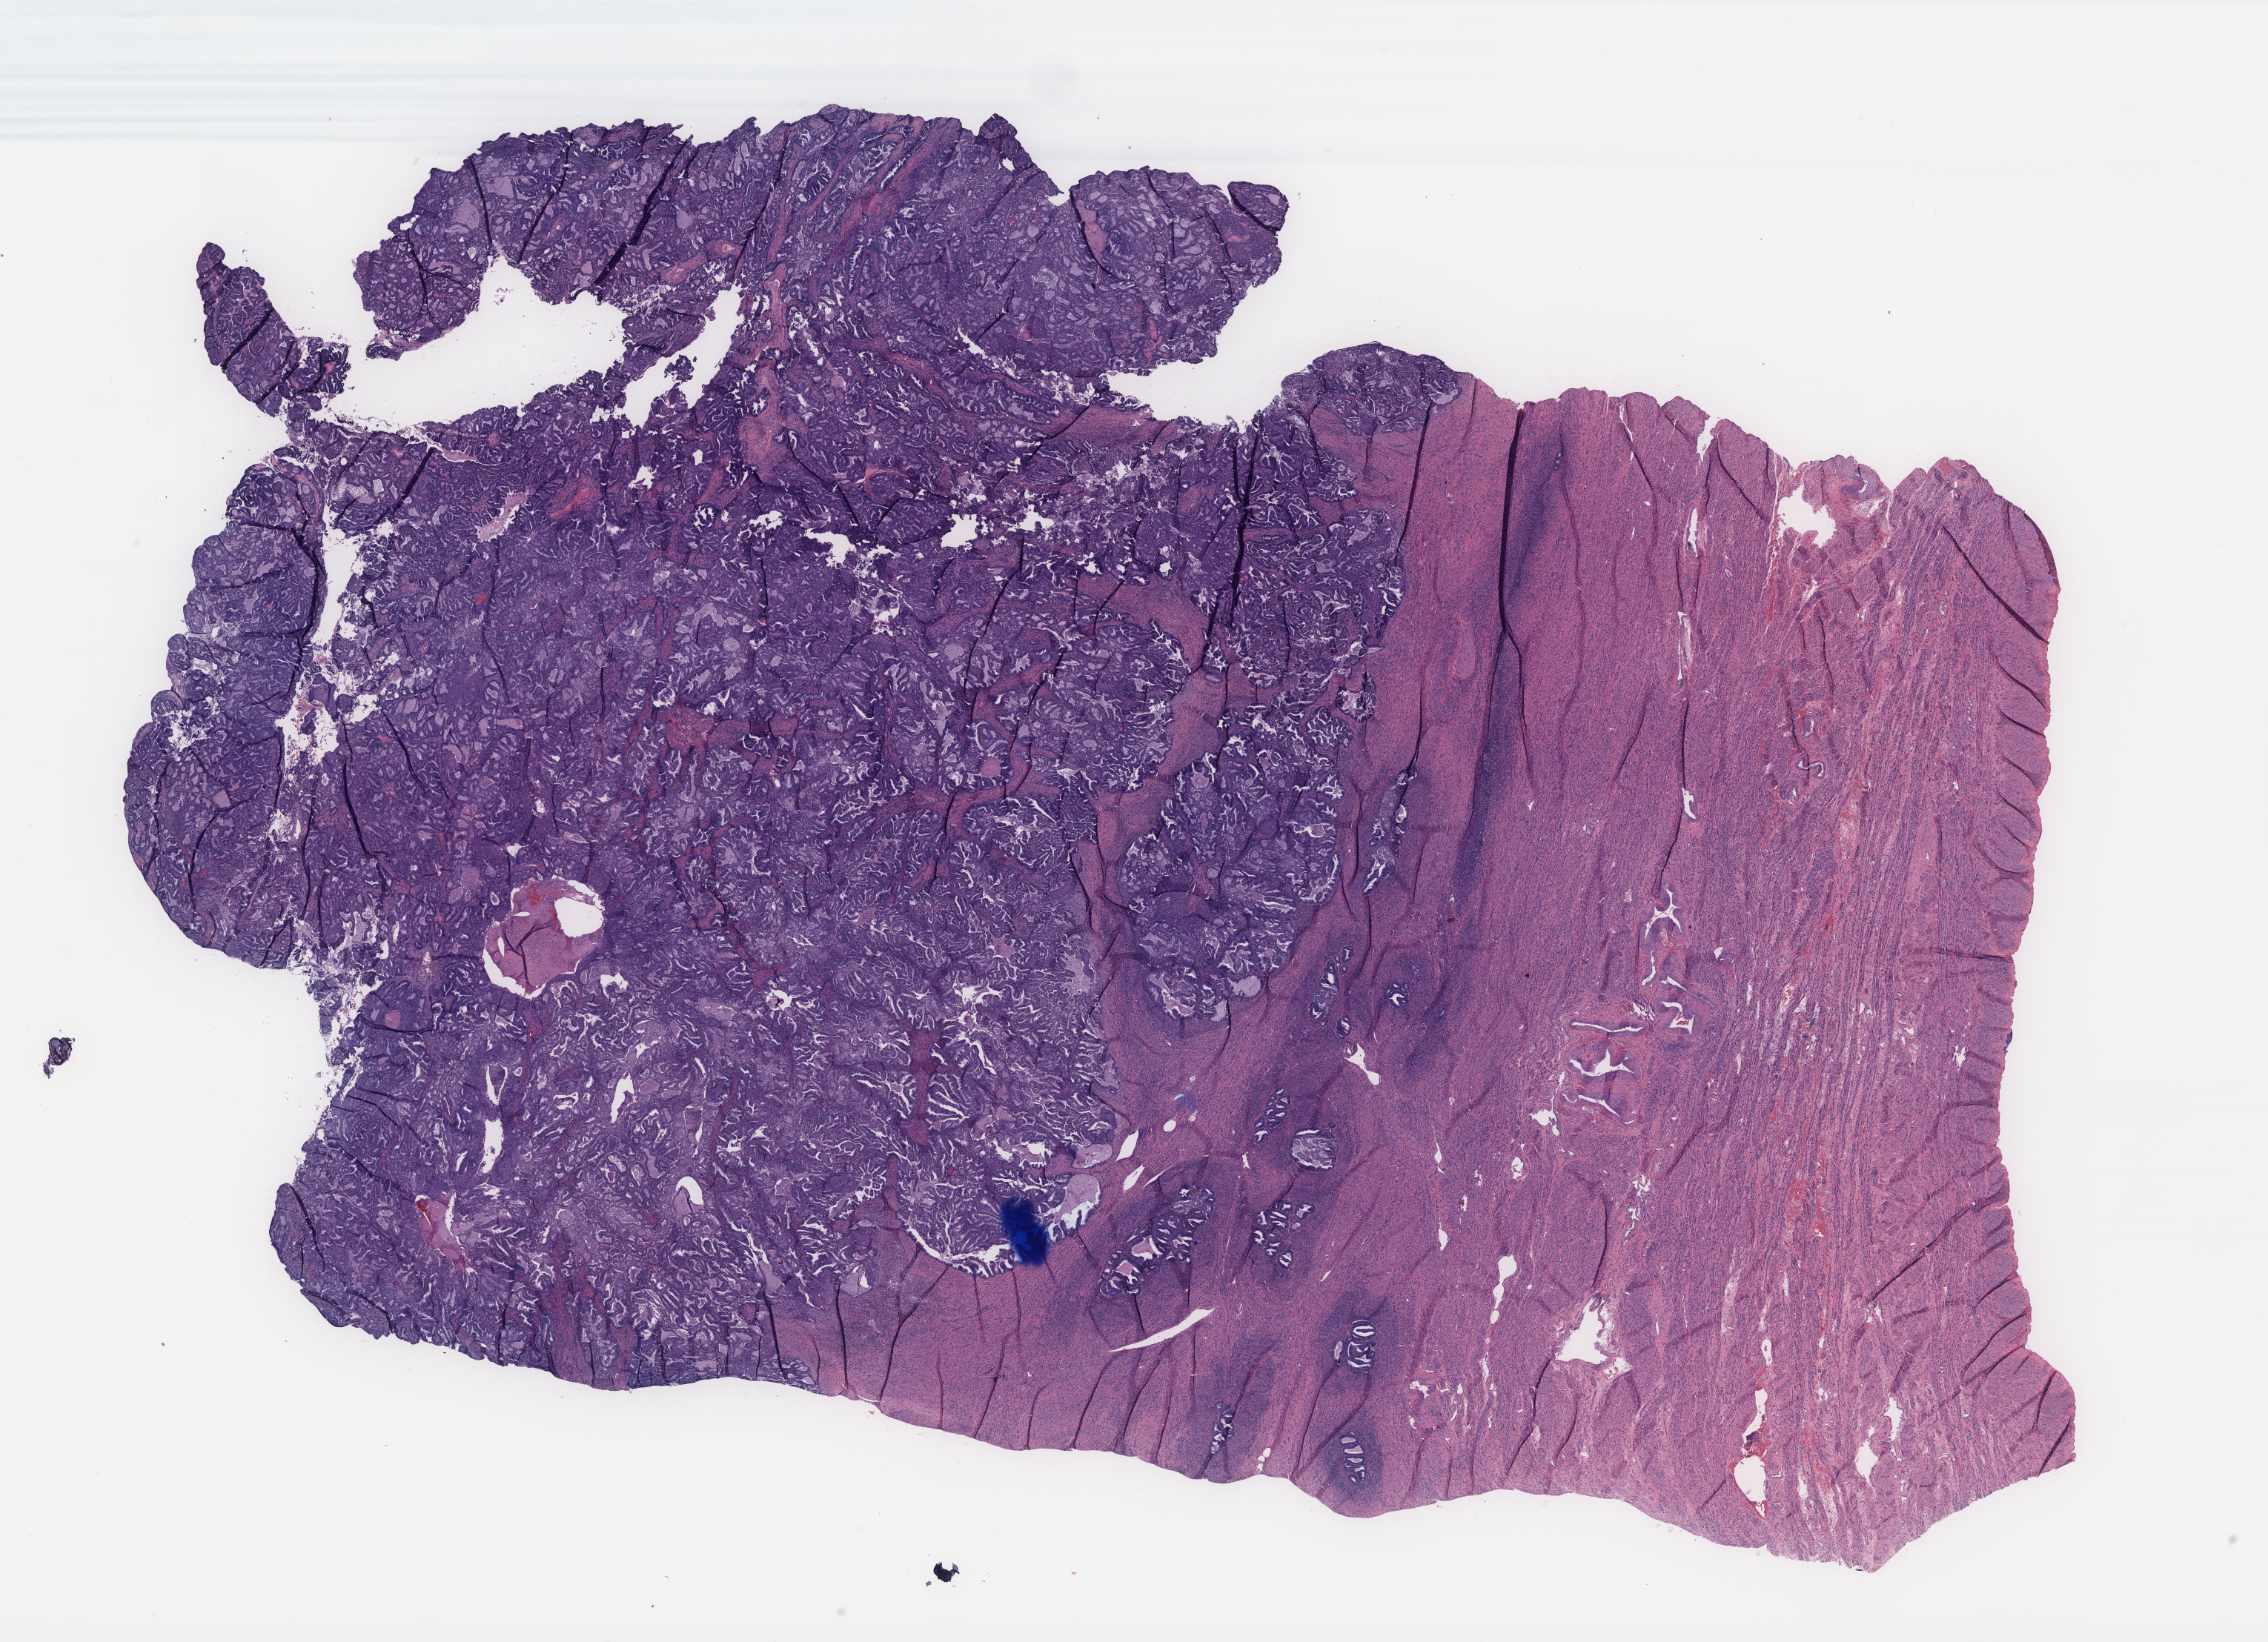
Digitized H&E tissue section (whole slide), low-resolution overview of the scanned area, about 24.5 x 17.8 mm; FFPE section; uterus, primary tumour sample. Female patient; age at initial diagnosis 78 years. Histologic grade: G1 (well differentiated).
FIGO stage: IIIA. Diagnosis: Endometrioid adenocarcinoma, NOS (endometrium).